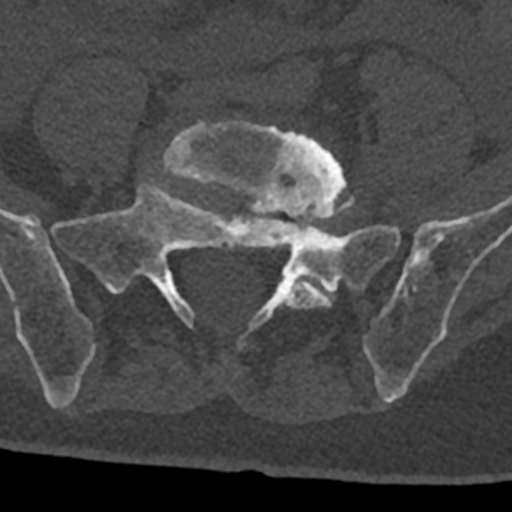
CT including the spine, one axial slice. Position 169 of 797 along the scan axis. Bone window (W 1800 / L 400 HU). 512 × 512 image matrix, field of view 160 × 160 mm. Male patient, age 74 years. From the clinical record (not read from this slice): primary cancer: renal; vertebrae with lytic lesions (as recorded): T10, L1, L2, L3, L4, L5.
Structures marked on this image (semi-automatic segmentation, software-assisted and operator-edited):
- L5 vertebra: bounding box <162,121,350,362> (left, top, right, bottom; pixels)